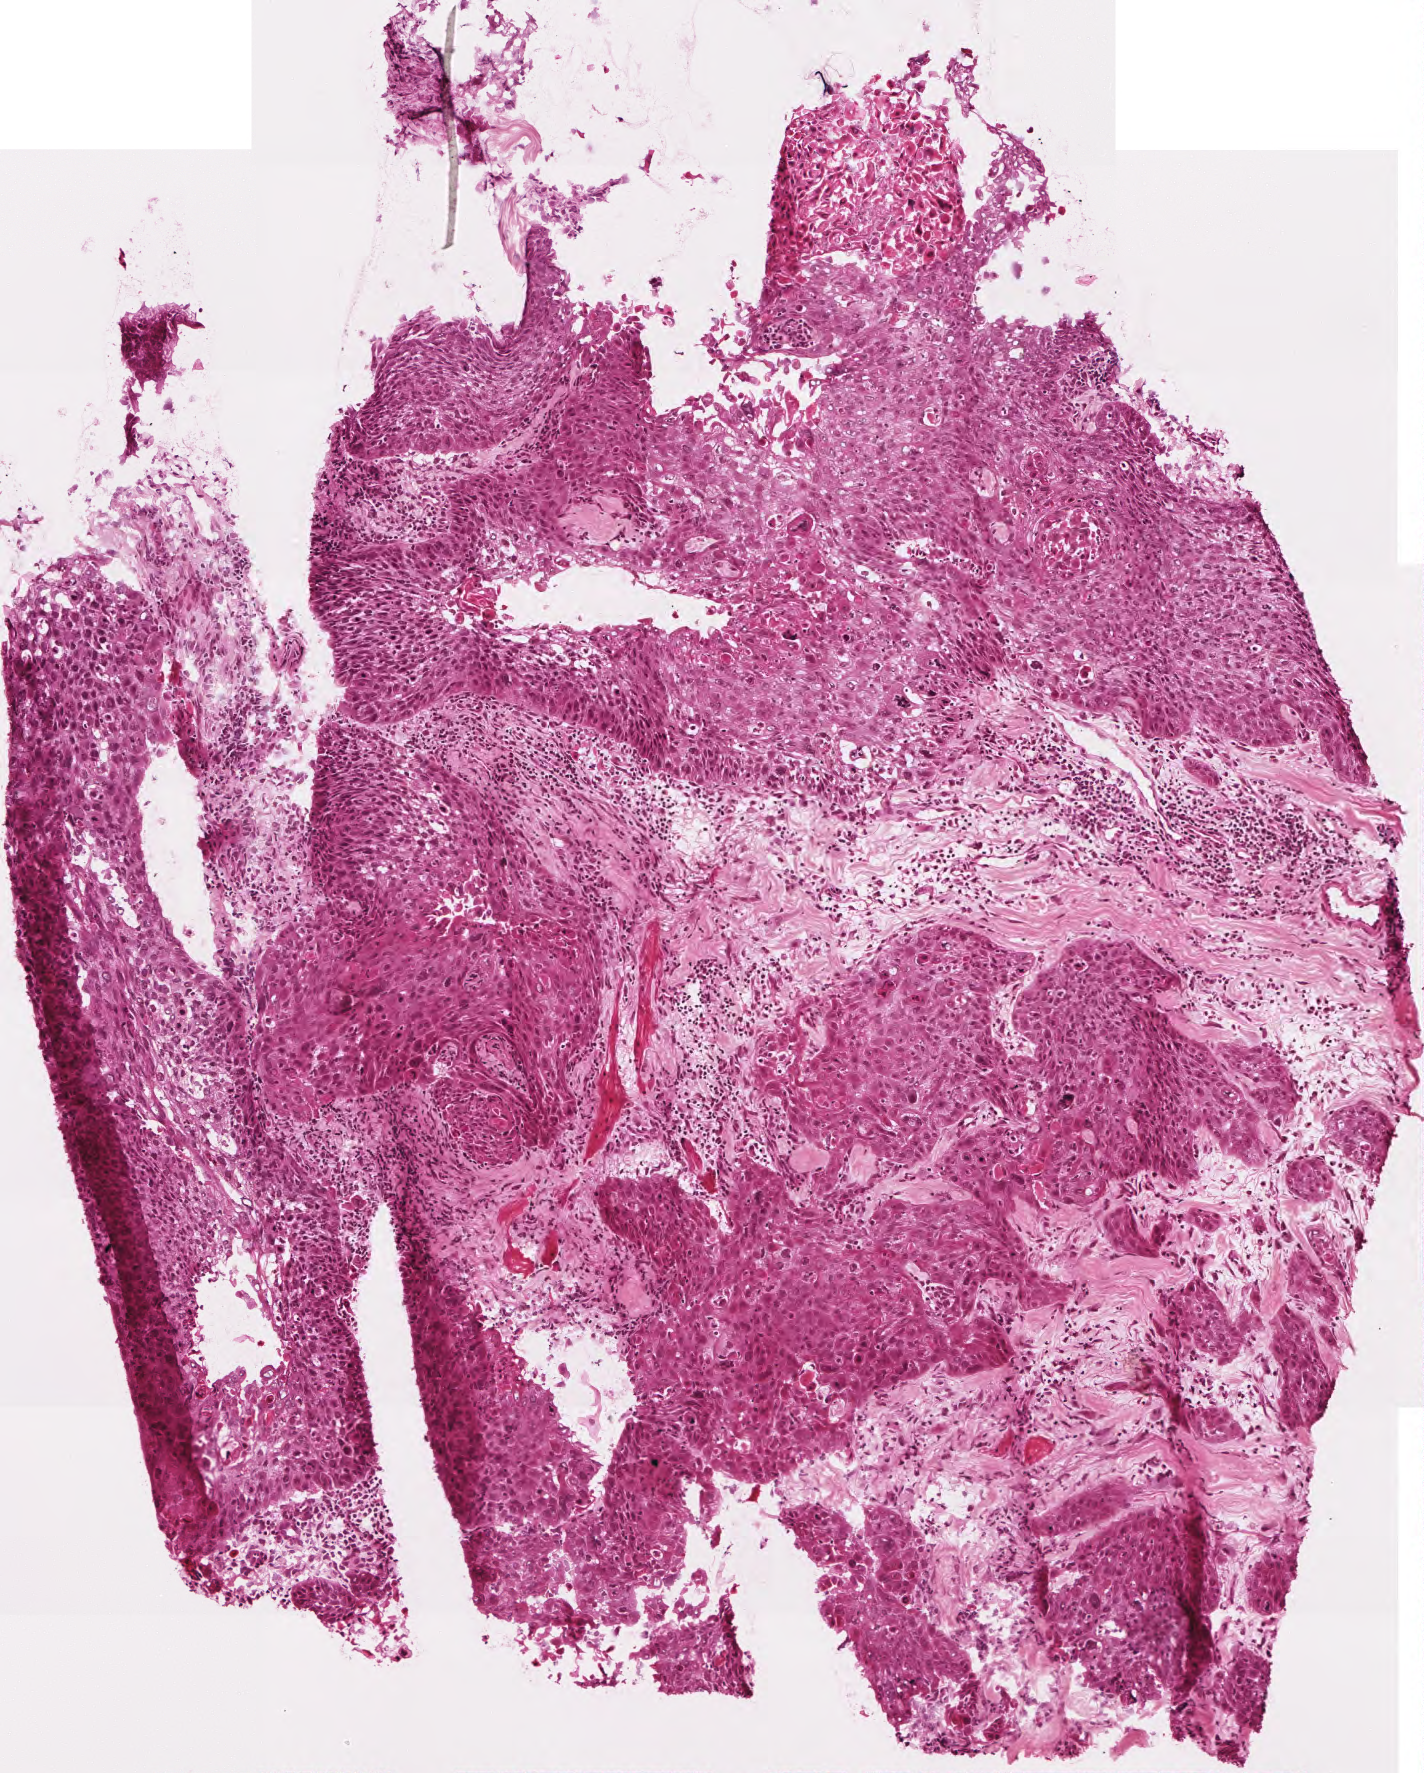
H&E whole-slide image, shown as a low-resolution overview of the whole scanned area (about 2.8 x 3.5 mm), frozen section from the top of the tissue portion, primary tumour sample from the head and neck. Patient: male, age at initial diagnosis 59 years. Histologic grade: G2 (moderately differentiated). Pathologist review of this section (percent, as recorded): tumour cells 75%, tumour nuclei 70%, normal cells 0%, stromal cells 25%, necrosis 0%.
* AJCC pathologic stage: IVA
* laterality: right
* pathologic diagnosis: Squamous cell carcinoma, NOS